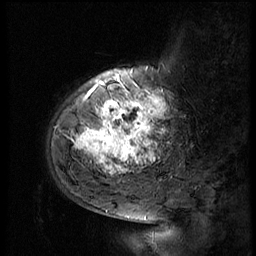
Breast MRI (dynamic contrast-enhanced), one sagittal slice; 3 images stored at this slice position (order not interpretable as contrast timing); 1.5 T; TE 4.2 ms, TR 9 ms; 256 × 256 image matrix. Female patient, age 51 years. Case-level facts recorded for this patient, not image findings: setting: breast cancer imaged before/during neoadjuvant chemotherapy; receptor status: triple-negative.
Annotated regions visible in this slice (semi-automatically segmented with operator editing):
- analysis volume of interest (the breast-tissue region the enhancement analysis was run in; not a lesion): bounding box (x1, y1, x2, y2) in pixels: (52, 66, 183, 179)
- tumour enhancement mask (voxels above the 140 % enhancement threshold inside the analysis volume of interest): (74, 82, 166, 173)